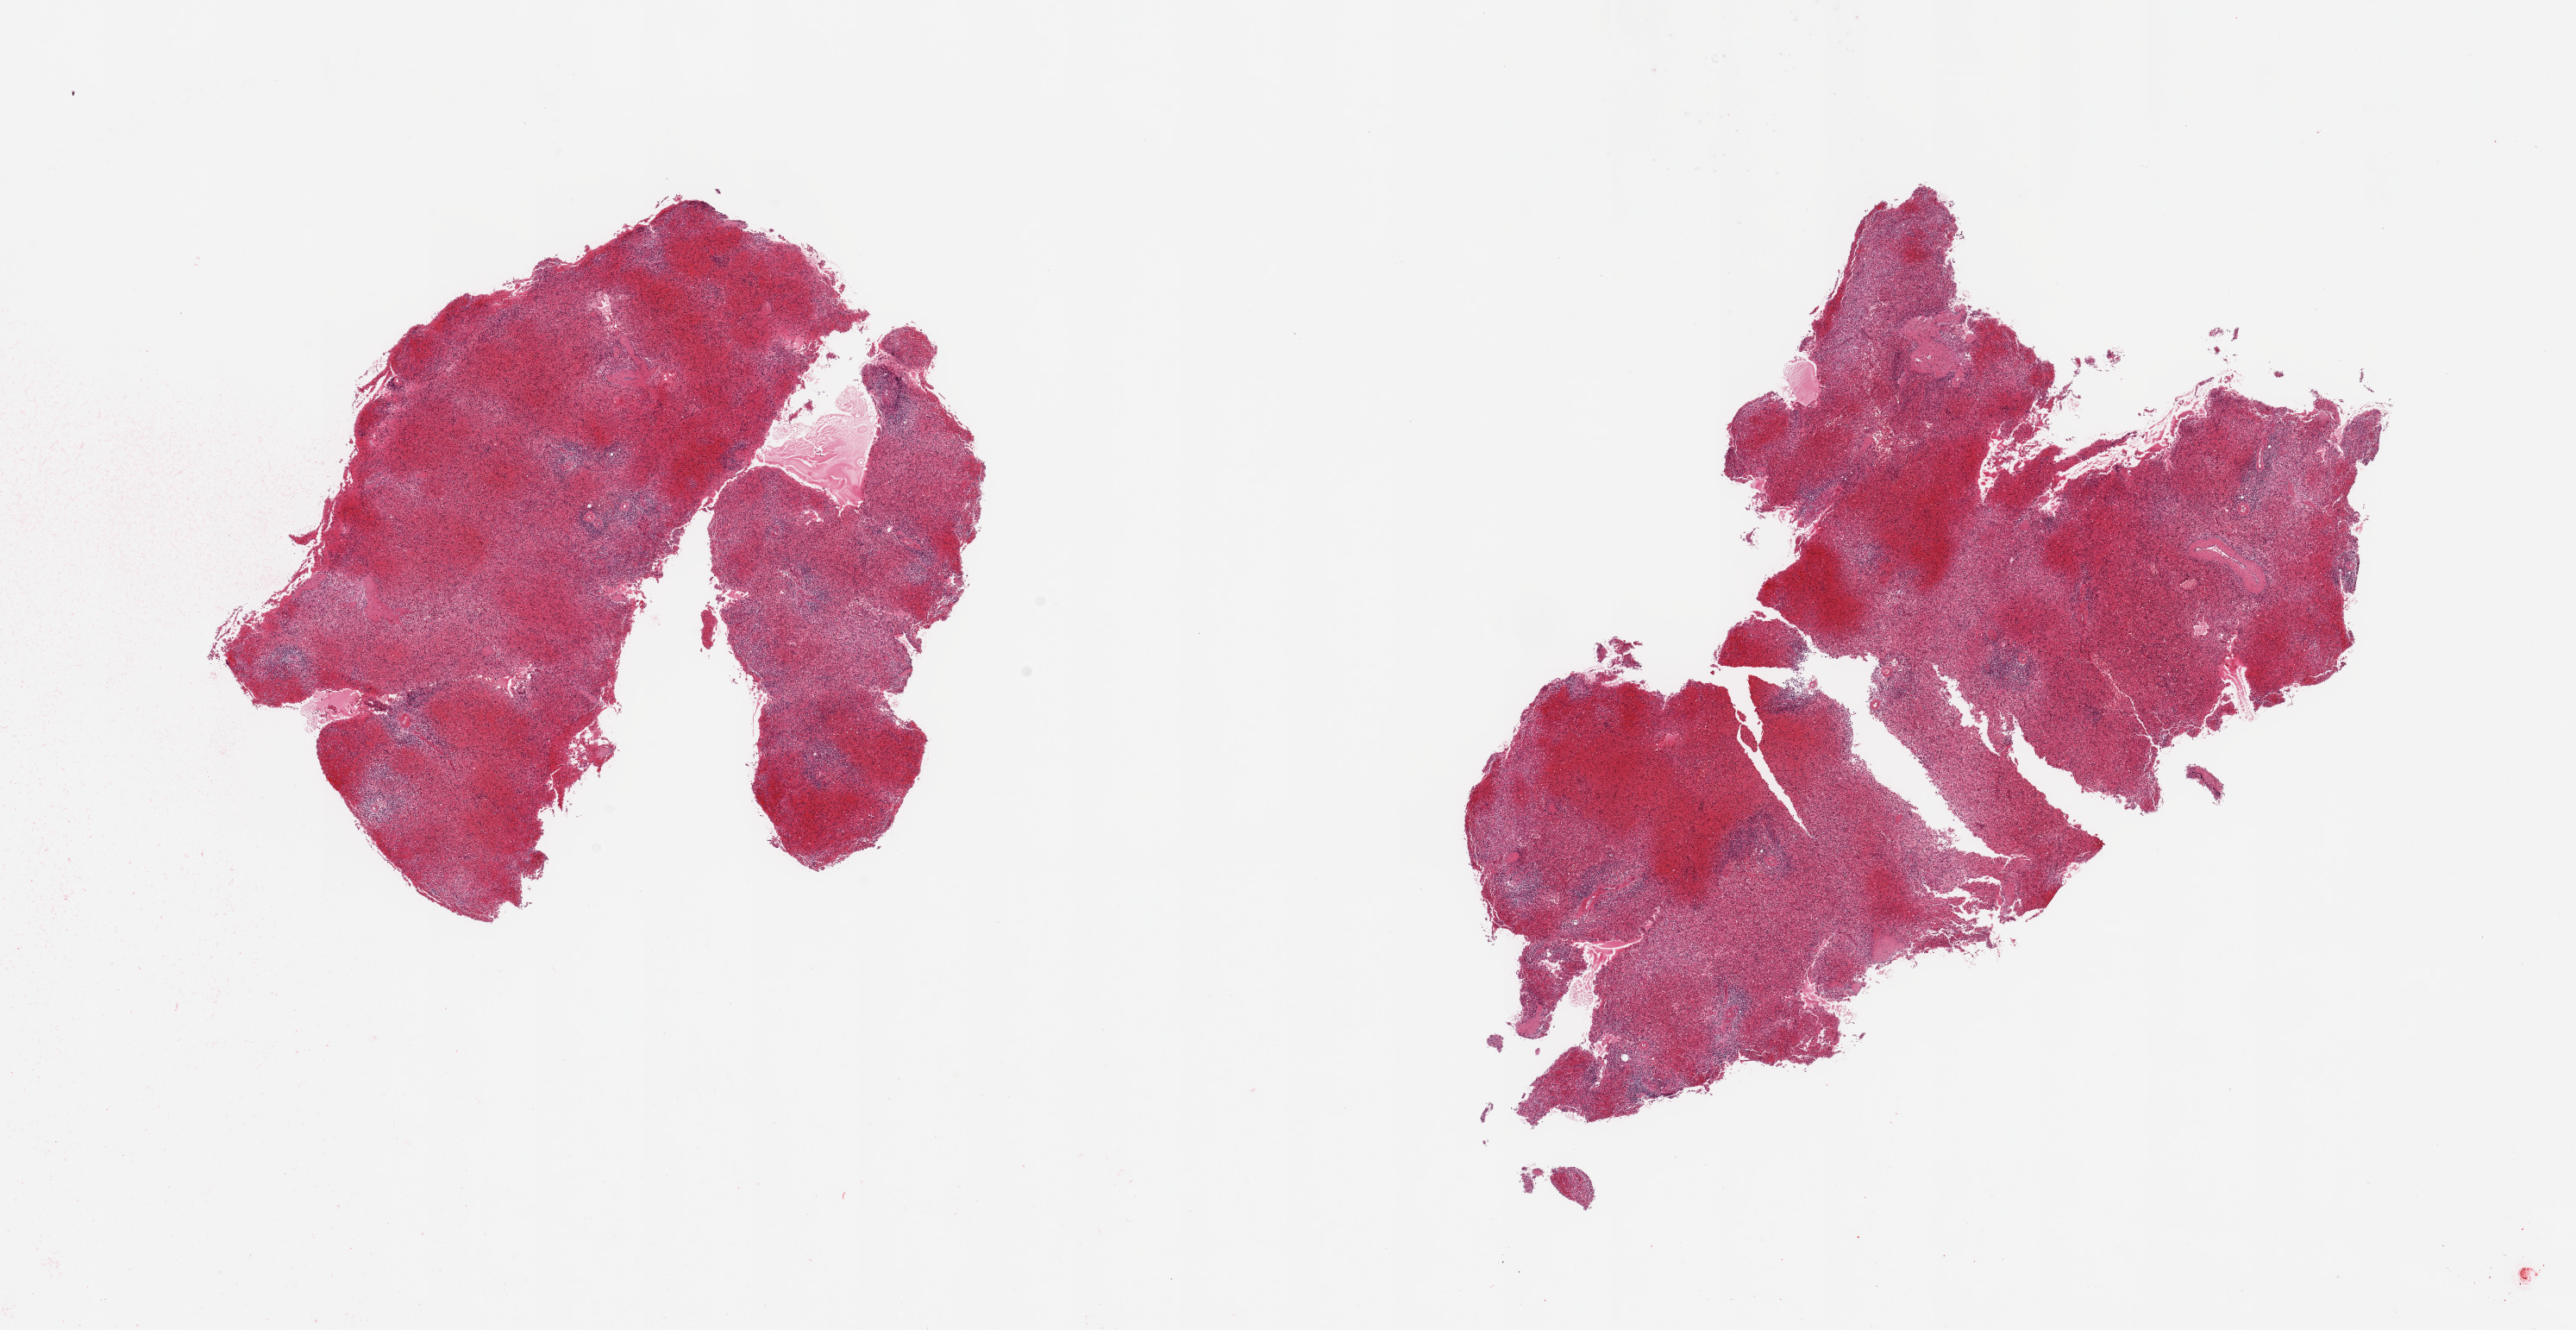
H&E whole-slide image, low-resolution overview of the scanned area, about 23.6 x 12.2 mm. PAXgene-fixed paraffin-embedded (PFPE) section. Section of spleen (target tissue). Tissue donor sample. Female donor.
Pathologist's review note for this sample: 2 pieces; severe congestion.